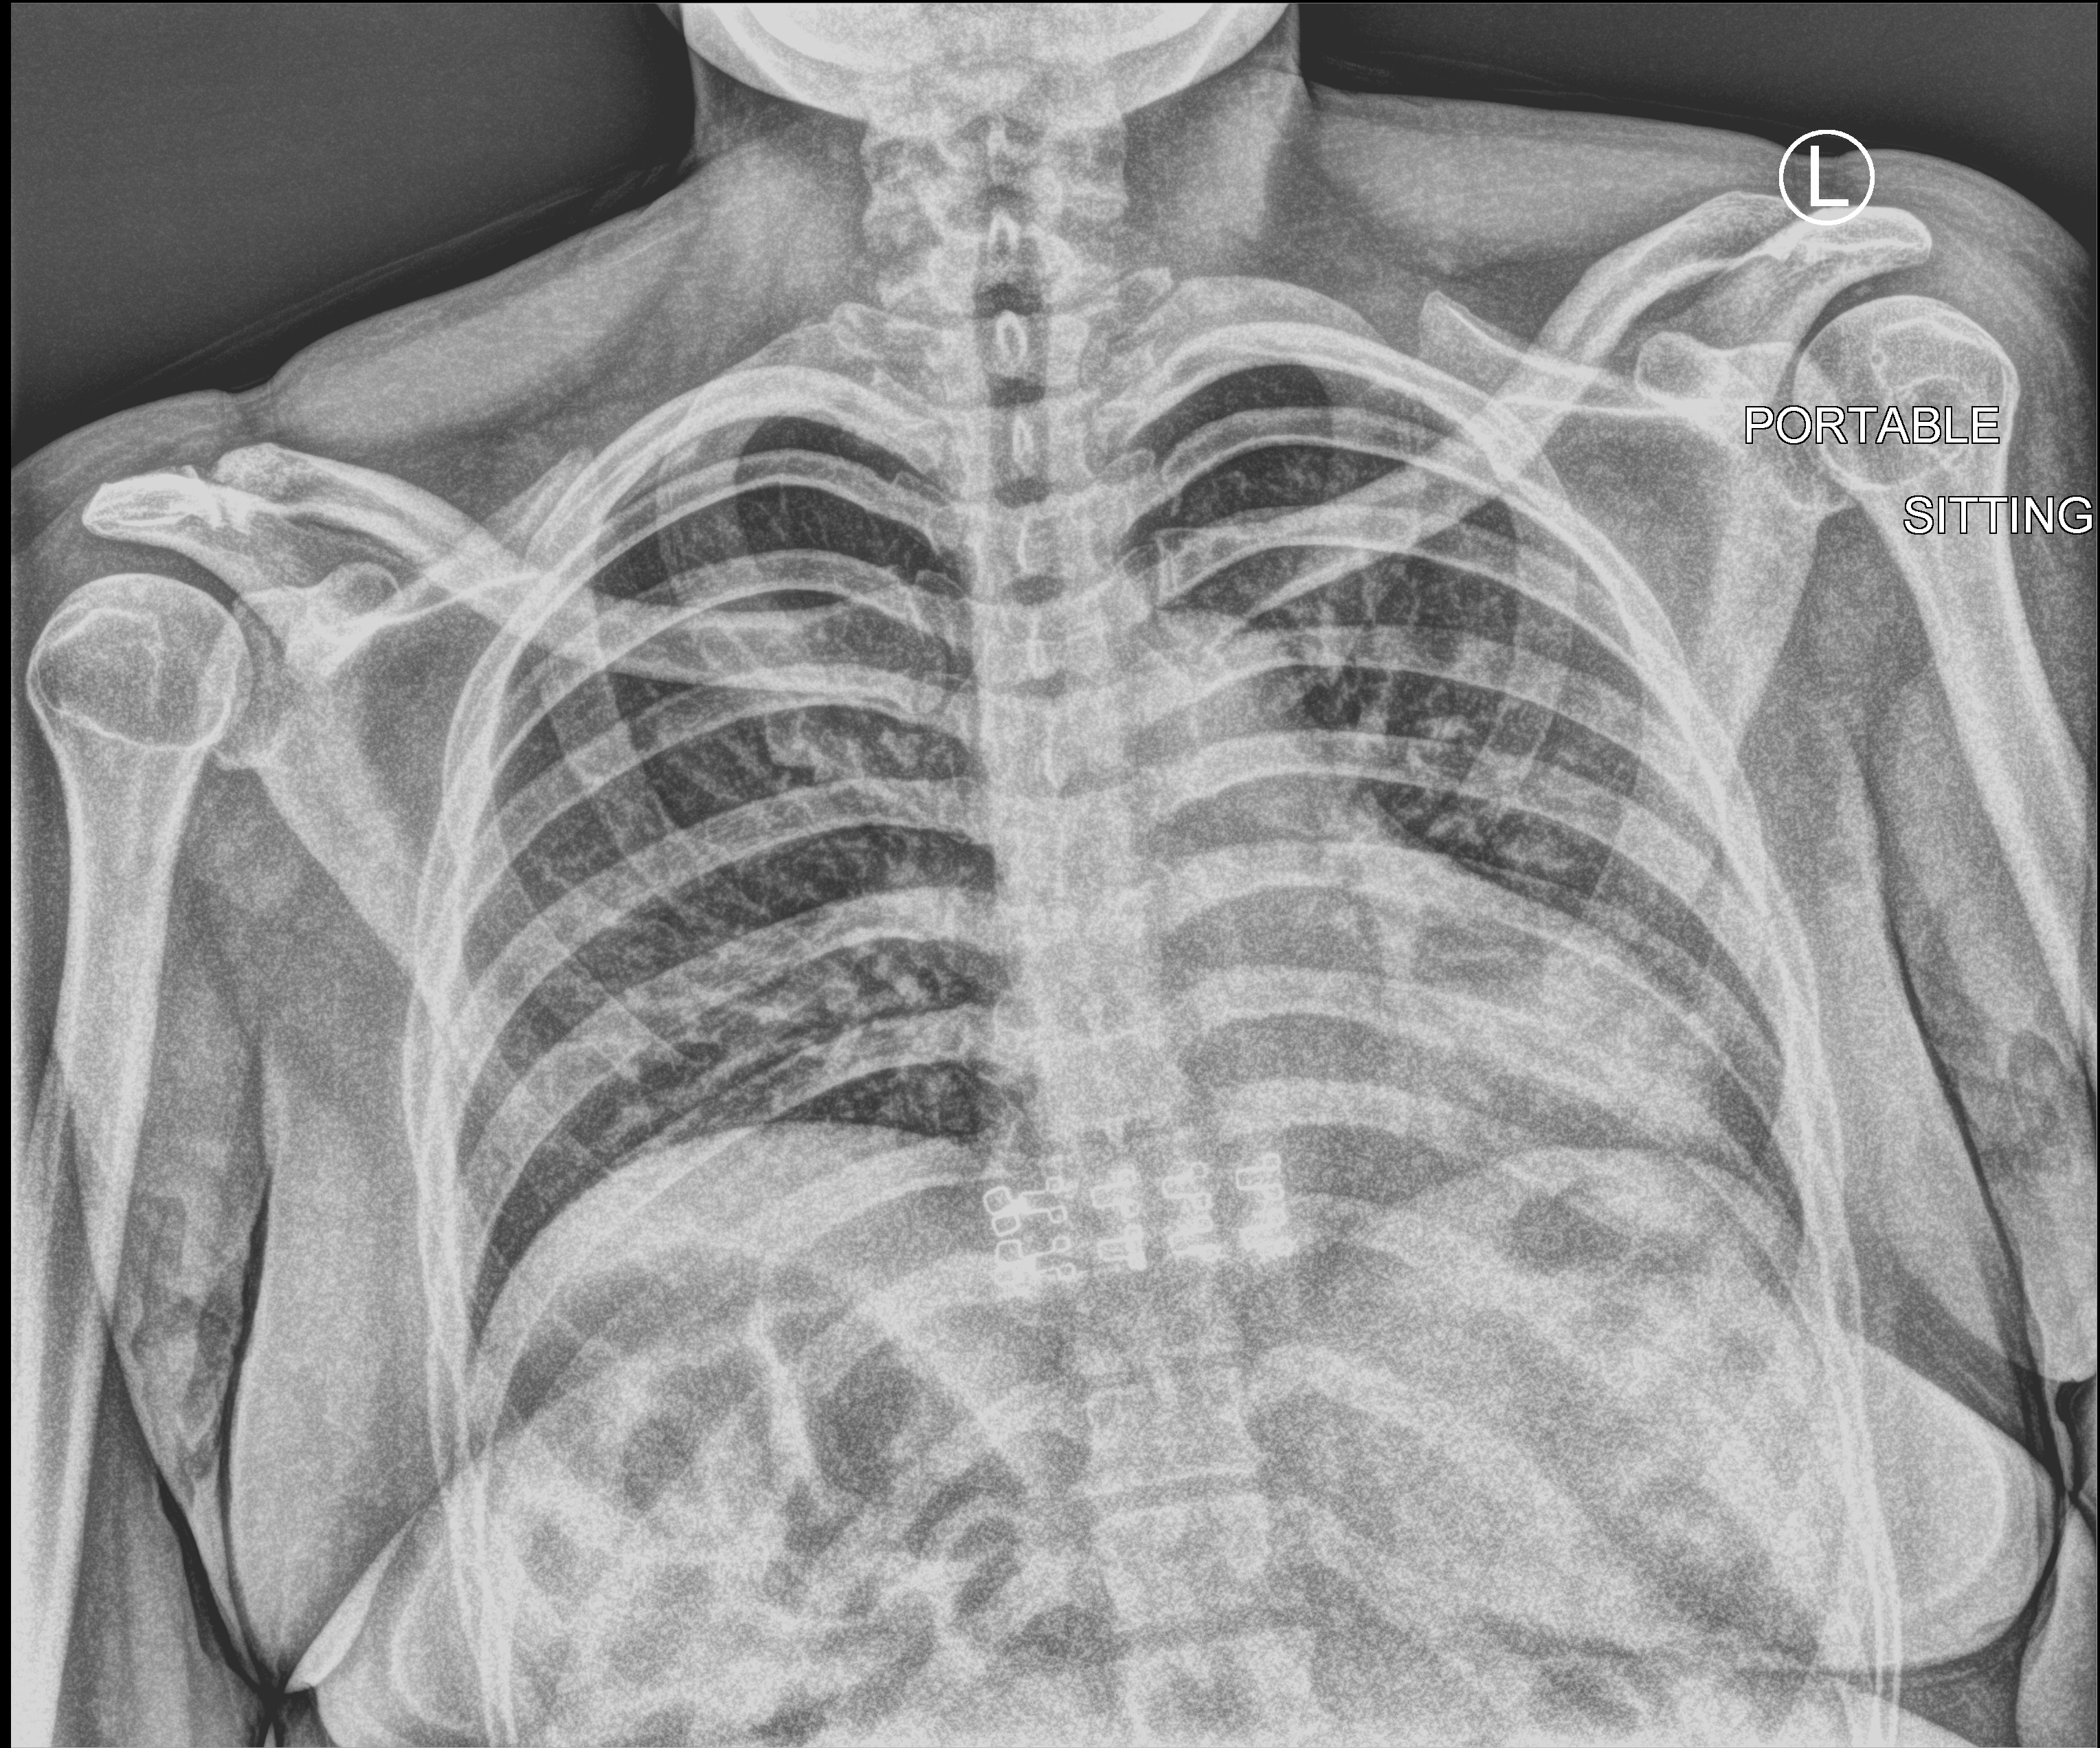
Chest X-ray (portable), anteroposterior (AP) projection. Patient hospitalised with COVID-19; female, aged 18–59 years.
From the hospital-stay record, not from the radiograph (when in the stay this image was taken is not recorded):
- hypertension (admission record): no
- COPD (admission record): no